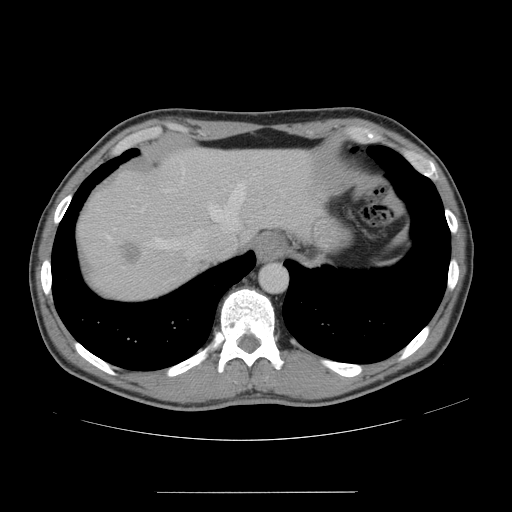
Contrast-enhanced abdominal CT, one axial slice. Slice 129 of 178 in the series (ordered by position). Intravenous contrast given. Soft-tissue window (W 400 / L 40 HU). 2.5 mm slice thickness. 512 × 512 image matrix. Male patient, age 53 years. From the clinical record (not read from this slice): diagnosis: colorectal cancer liver metastases, imaged before liver resection; multiple liver metastases: yes; largest metastasis: 2.4 cm; disease in both lobes: no.
Annotated regions visible in this slice (manually delineated by an expert):
- hepatic veins: bounding box (x1, y1, x2, y2) in pixels: (107, 183, 246, 256)
- liver: (78, 149, 312, 299)
- planned liver remnant (the part of the liver to remain after resection): (168, 149, 314, 239)
- liver metastasis: (121, 242, 143, 265)